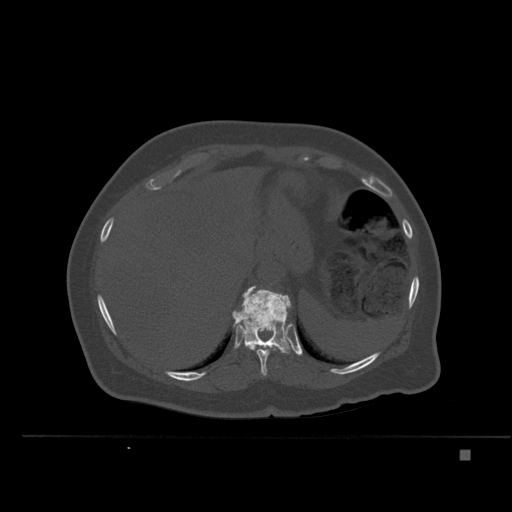
CT including the spine, one axial slice. Bone window (W 1800 / L 400 HU). 1.5 mm slice thickness. 512 × 512 image matrix. Female patient, age 74 years. From the clinical record (not read from this slice): primary cancer: colon.
Structures marked on this image (semi-automatic segmentation, software-assisted and operator-edited):
- T10 vertebra: bounding box (x1, y1, x2, y2) in pixels: (245, 343, 281, 376)
- T11 vertebra: (232, 286, 291, 354)